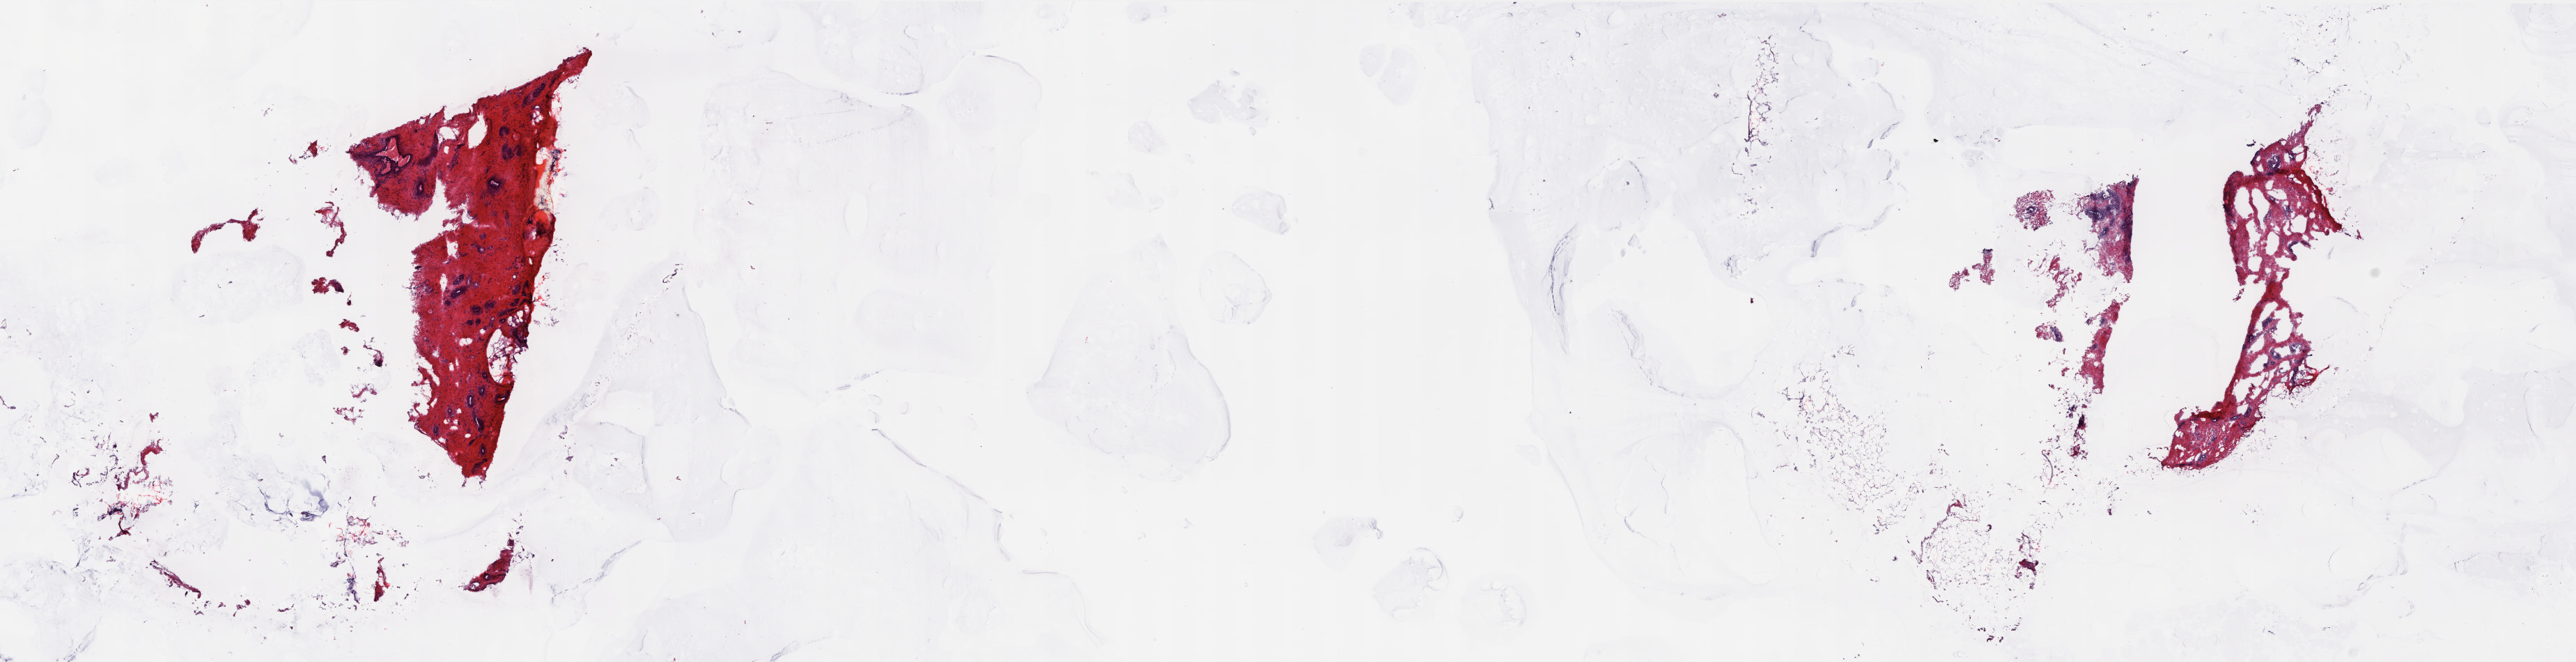
Whole-slide histology image, H&E, a low-resolution overview of the entire scanned area, about 29.8 x 7.7 mm (slide scanned at 20x); frozen section; sample: solid tissue normal (non-tumour tissue), breast. Female, age 62 years at initial diagnosis. Slide review estimates, as recorded: tumour cells 0%, tumour nuclei 0%, normal cells 15%, stromal cells 85%, necrosis 0%. Inflammatory infiltration, as recorded: lymphocyte infiltration 1%, monocyte infiltration 0%, neutrophil infiltration 0%.
This section: solid tissue normal sample (biorepository sample class). Patient diagnosis: Lobular carcinoma, NOS.